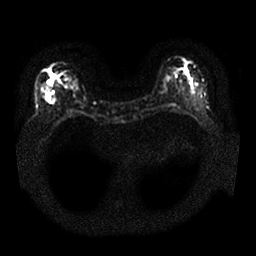
Breast MRI, one axial slice; position 7 of 25 along the scan axis; diffusion-weighted series; image 2 of 4 stored at this slice position (different b-values; order by instance number); 1.5 T; 4 mm slice thickness; 256 × 256 image matrix. Female patient.
Structures marked on this image (expert manual segmentation):
- tumour on diffusion-weighted imaging: bounding box <46,71,53,86> (left, top, right, bottom; pixels)